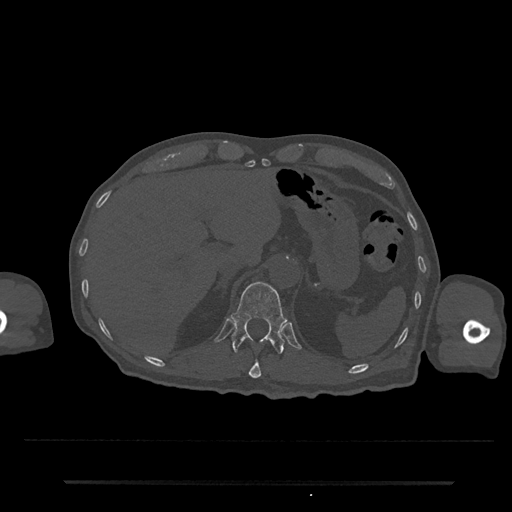
CT including the spine, one axial slice; slice 211 of 797 in the series (ordered by position); 120 kVp; bone window (W 1800 / L 400 HU); 512 × 512 image matrix. Patient: male, 74 years. Case-level facts recorded for this patient, not image findings: primary cancer: prostate.
Outlined on this slice (semi-automatic segmentation, software-assisted and operator-edited):
- T11 vertebra: bounding box (x1, y1, x2, y2) in pixels: (249, 359, 261, 379)
- T12 vertebra: (232, 281, 287, 355)